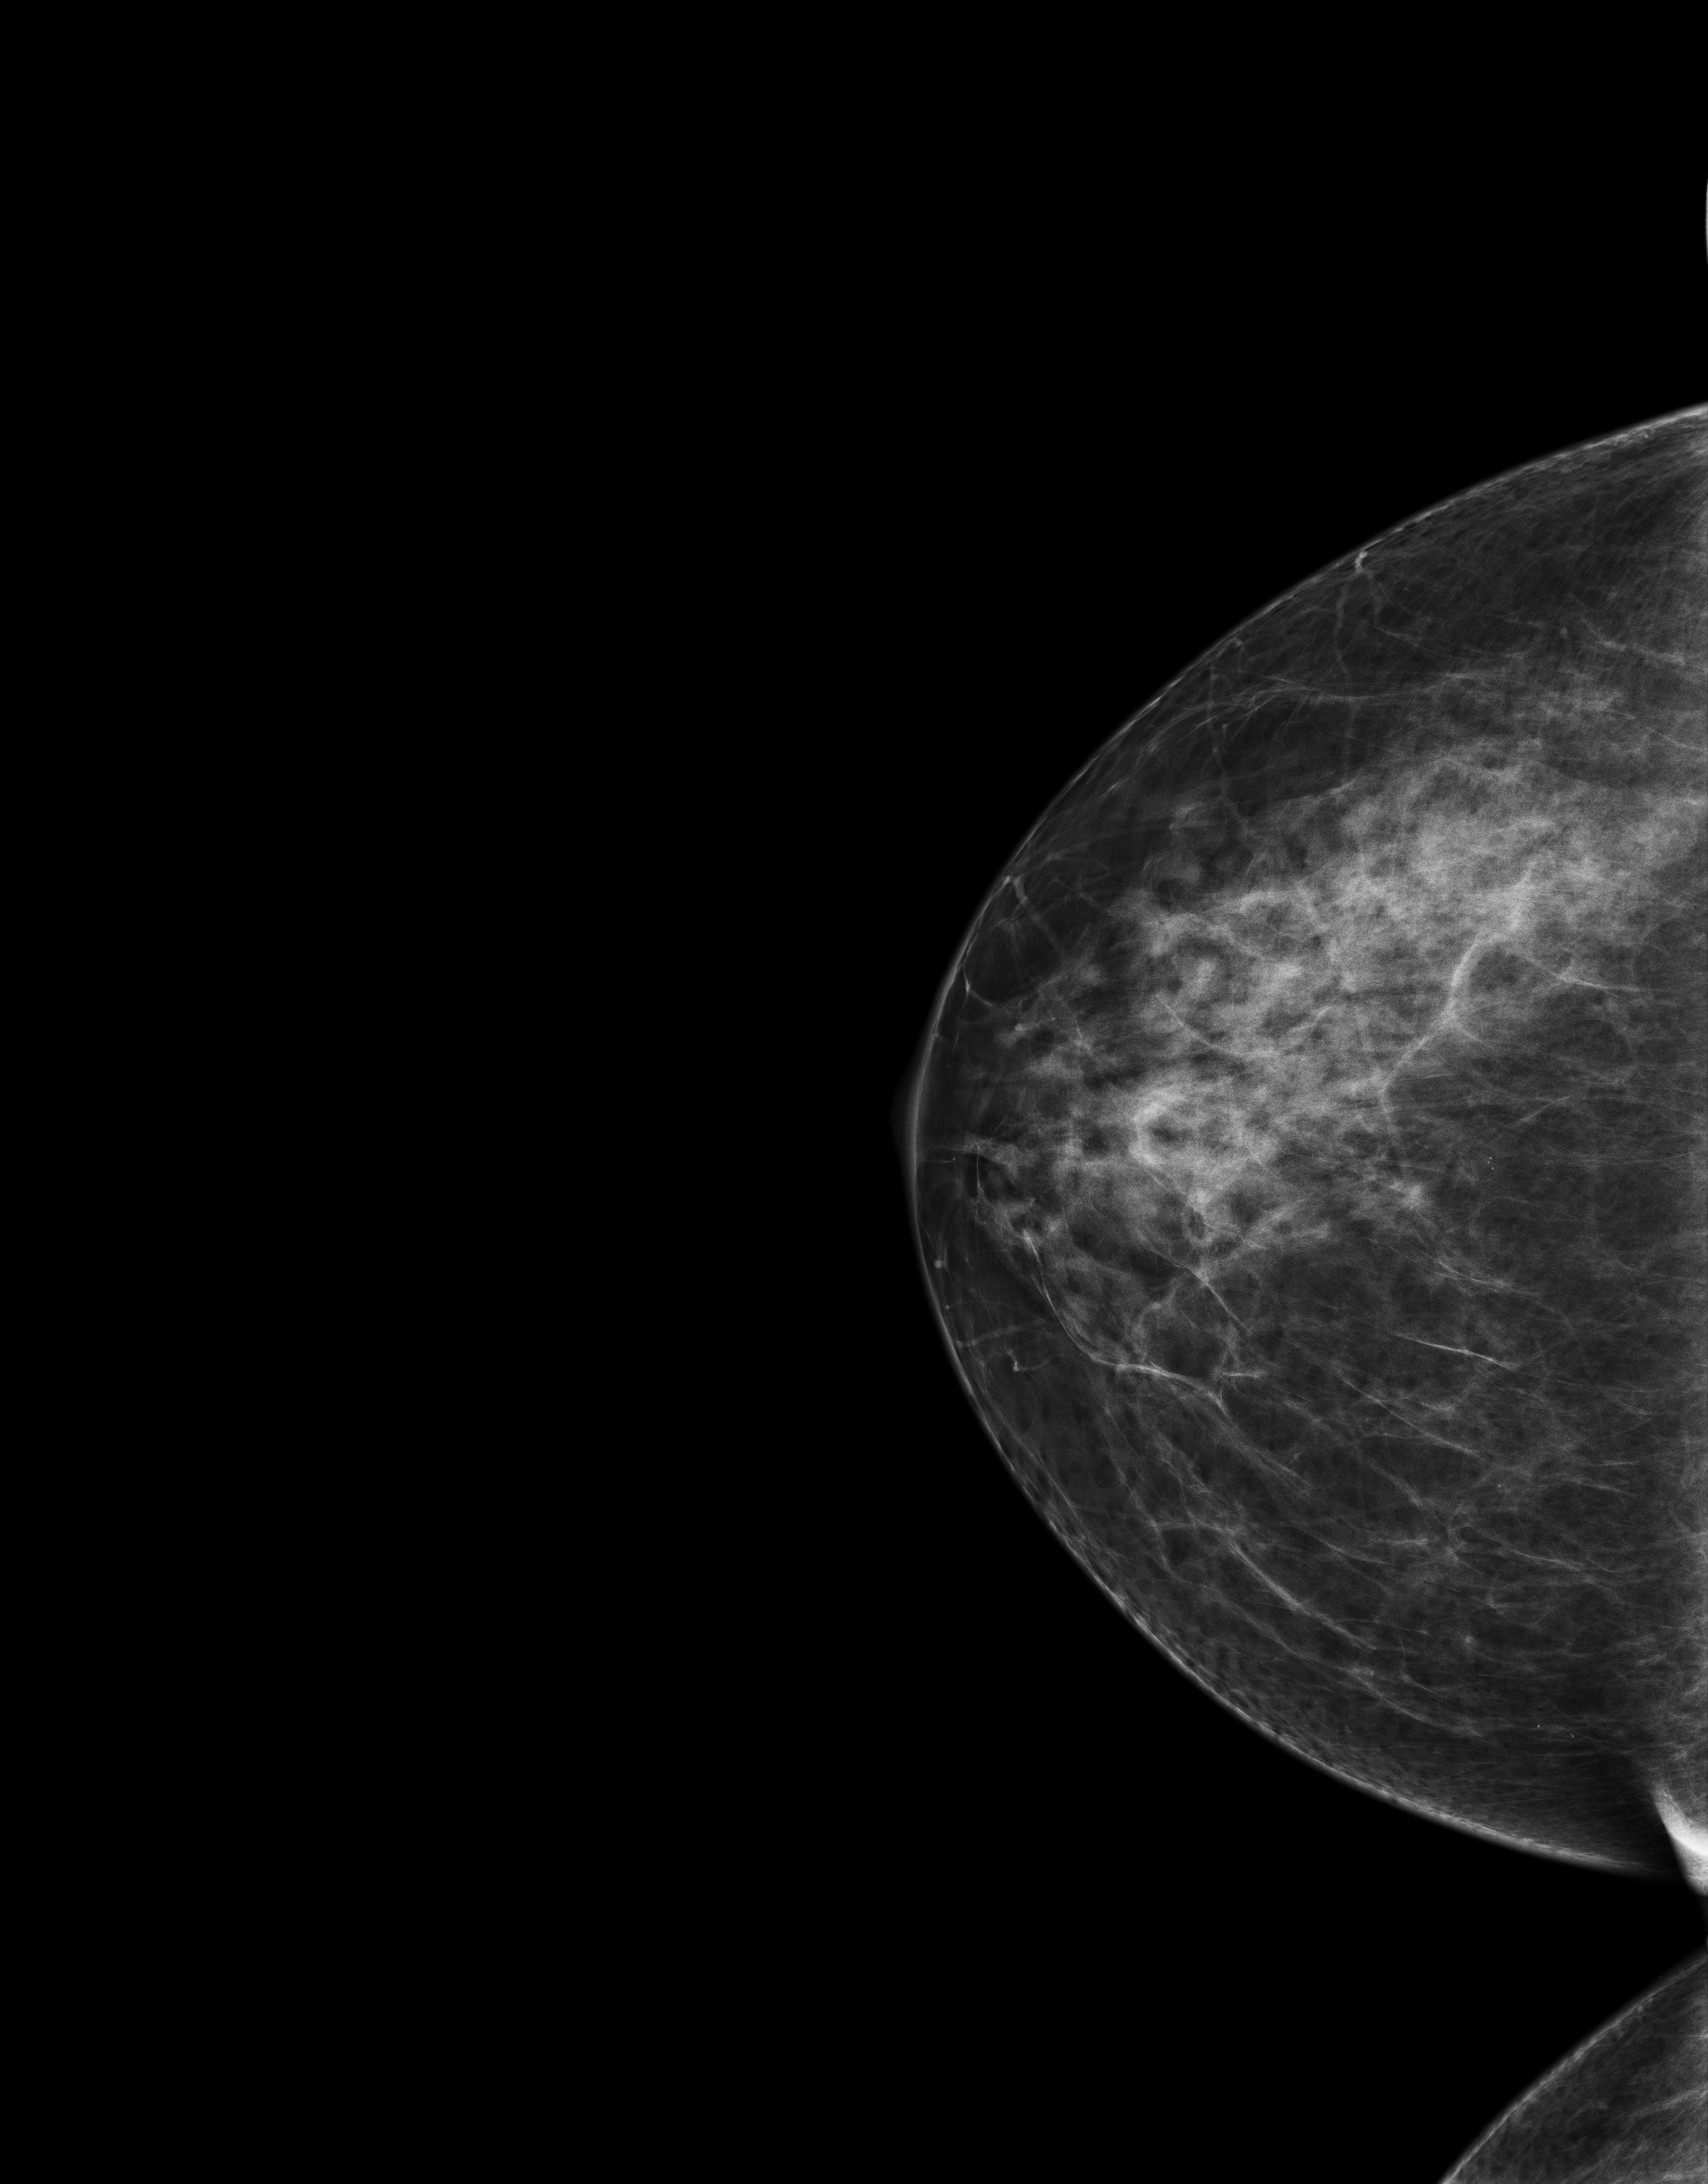
Full-field digital mammogram (FFDM), right breast, cranio-caudal projection, annual screening mammography examination, compressed breast thickness 67 mm. Patient: female, 57 years.
- breast density at the screening exam (both breasts): scattered fibroglandular densities (BI-RADS density category b)
- final BI-RADS category for the screening round (tomosynthesis exam, both breasts): category 1
- recall: no recall after this screen